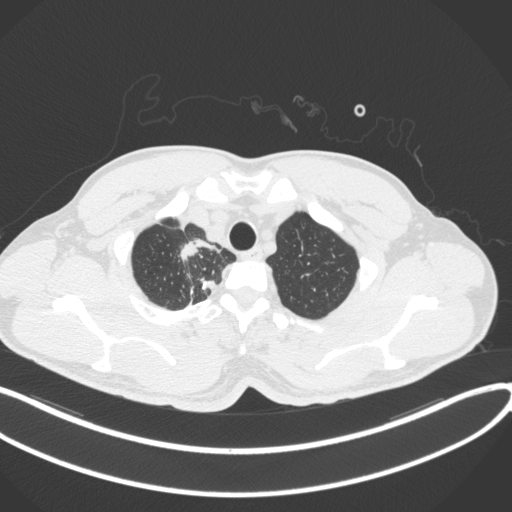
Chest CT, one axial slice. Position 334 of 391 along the scan axis. 120 kVp. Lung window (W 1500 / L -600 HU). 512 × 512 image matrix, field of view 400 × 400 mm. Male patient, age 48 years. Case-level facts recorded for this patient, not image findings: clinical TNM (as recorded): T1c N1 M1.
Structures marked on this image (bounding box drawn by a radiologist):
- lung tumour (recorded histology: adenocarcinoma): bounding box <180,236,222,268> (left, top, right, bottom; pixels)